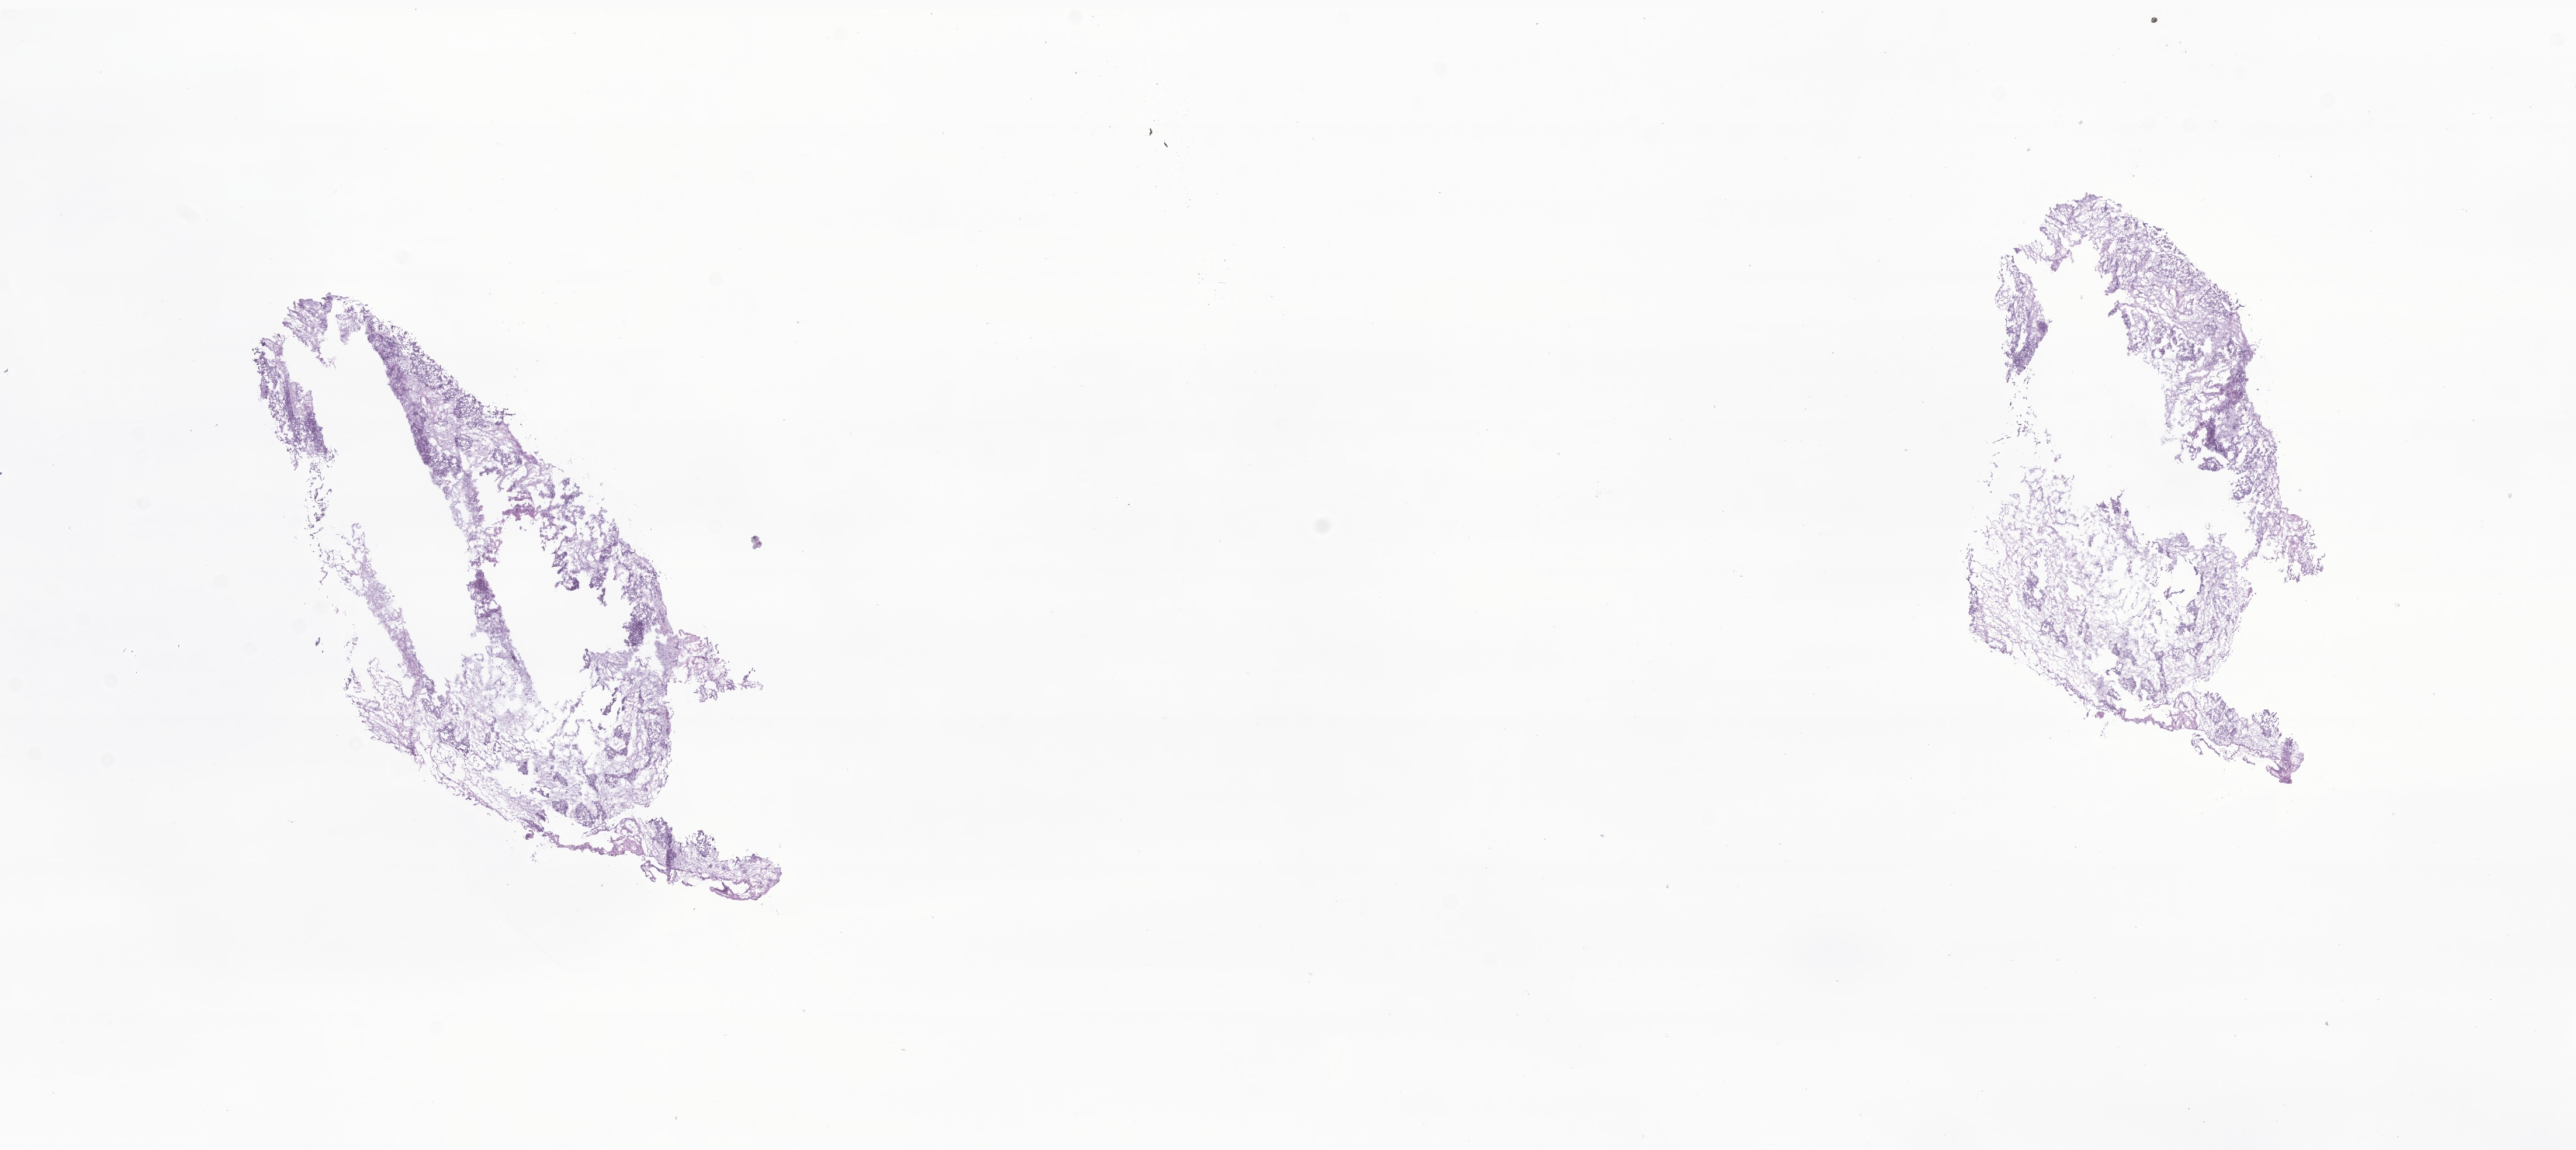
Hematoxylin and eosin (H&E) whole-slide image of tumor tissue from the abdomen — shown as a low-resolution overview of the whole scanned area (about 18.6 x 8.3 mm), cryosection (OCT / tissue freezing medium). Female patient, age 168 months (14 years).
• recorded diagnosis: Desmoplastic small round cell tumor